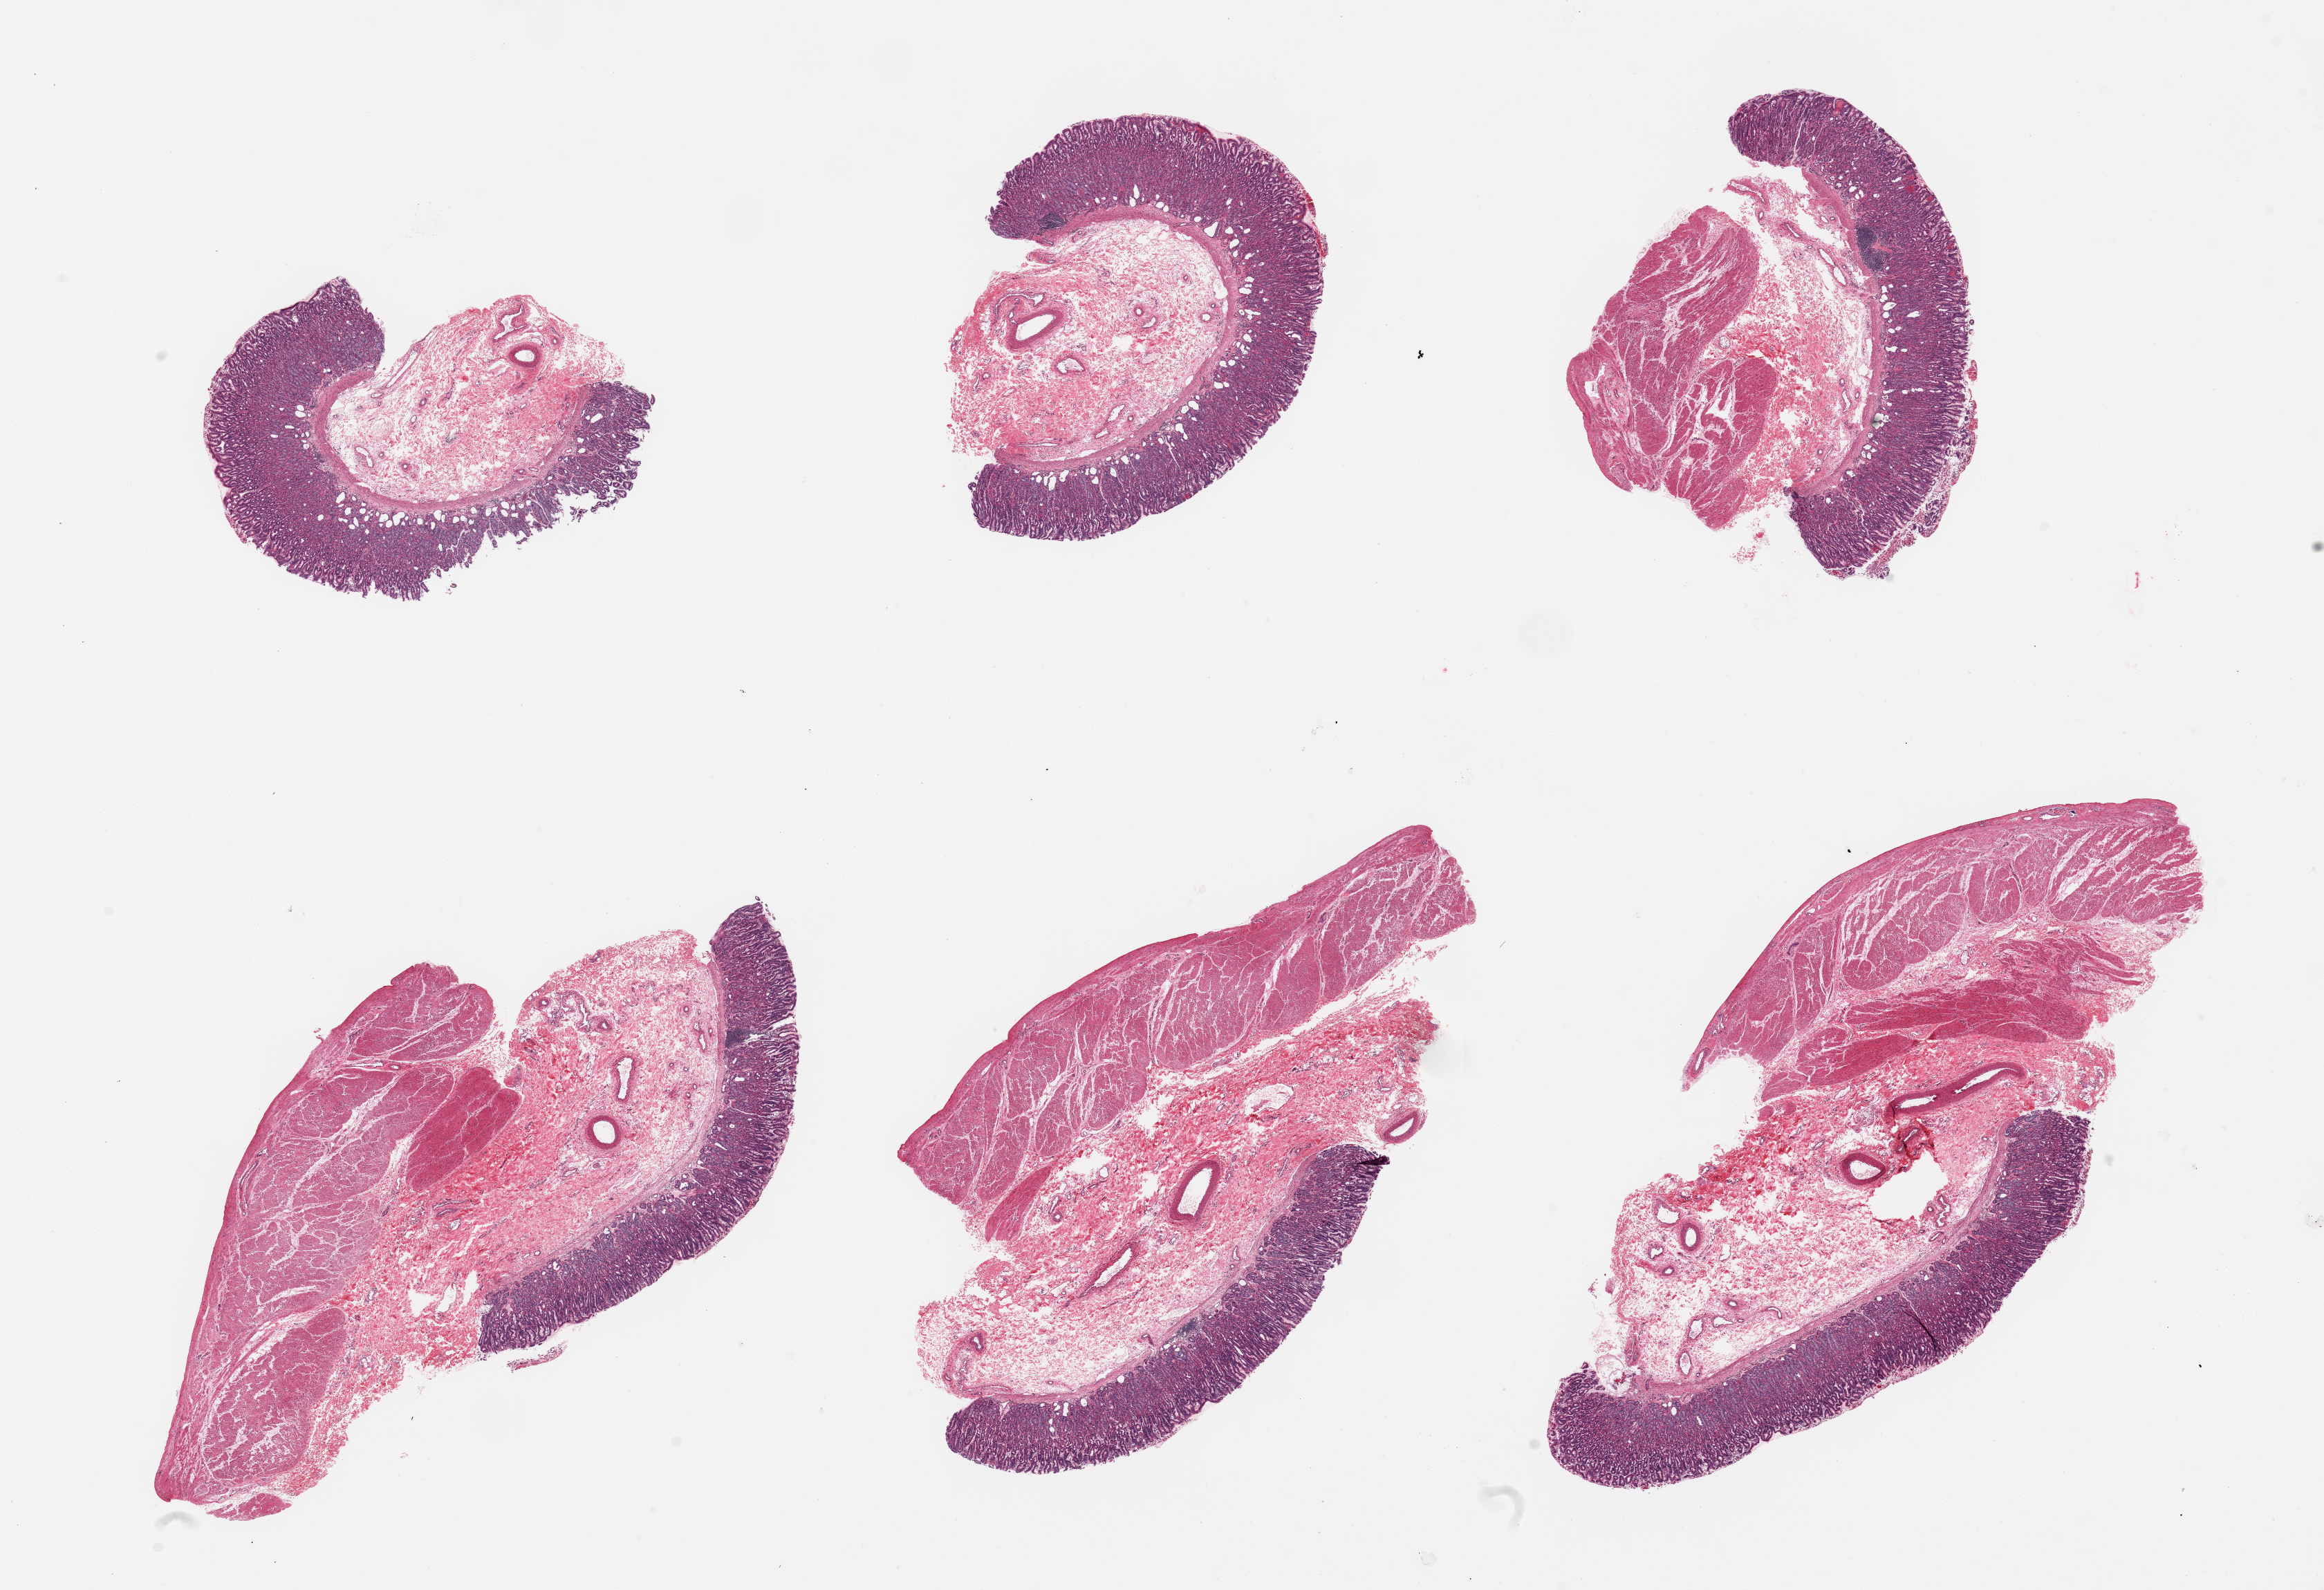
Hematoxylin and eosin (H&E) whole-slide image, brightfield — low-resolution overview of the scanned area, about 26.6 x 18.2 mm (slide scanned at 20x), PAXgene-fixed, paraffin-embedded tissue, section of stomach (target tissue), donor tissue sample. Donor: male.
- pathologist's review note for this sample: 6 pieces; 4 are full thickness, 2 have no muscularis